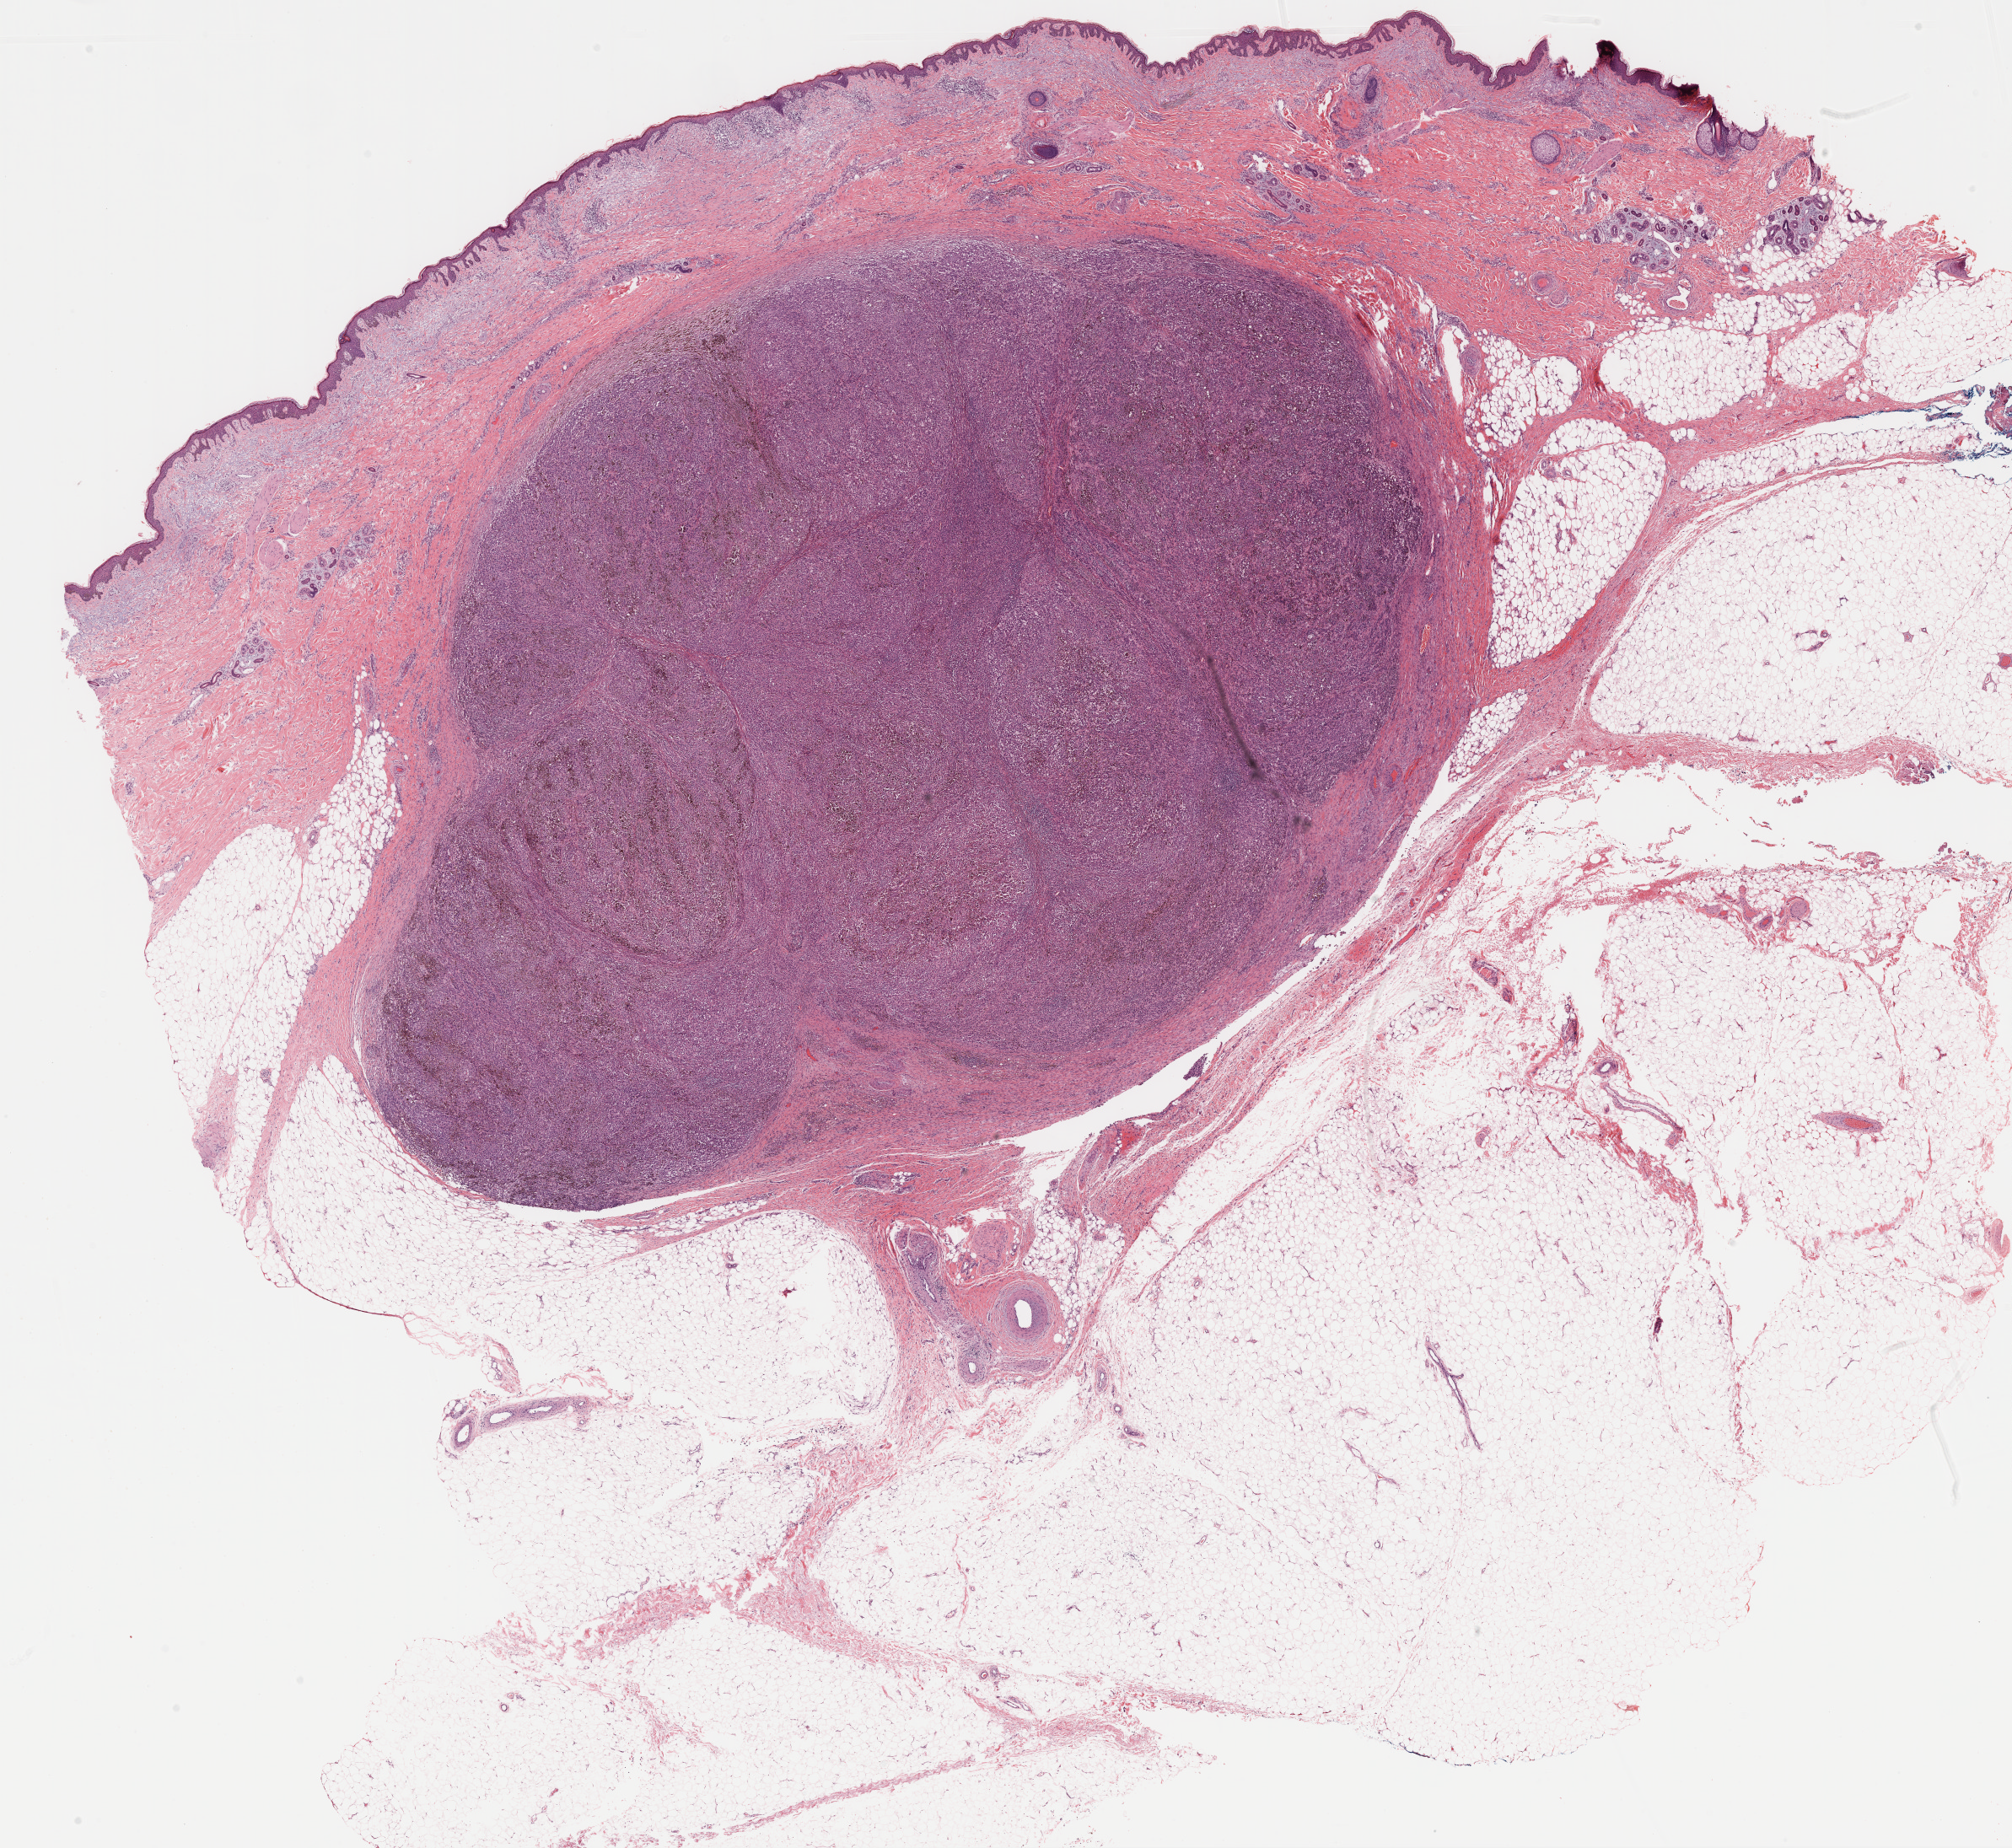
Hematoxylin and eosin (H&E) stained whole-slide image, shown as a low-resolution overview of the whole scanned area (about 19.2 x 17.7 mm, from a 20x scan); formalin-fixed paraffin-embedded (FFPE) diagnostic section; metastatic tumour sample, sampled site not recorded. Patient: male, age at initial diagnosis 61 years.
This section: metastatic tumour tissue. Patient diagnosis: Malignant melanoma, NOS.